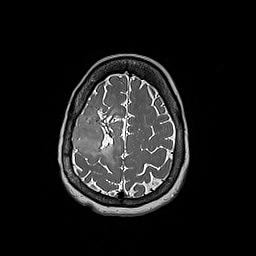
Brain MRI from a brain-tumour surgery series, one axial slice. Position 54 of 192 along the scan axis. 256 × 256 image matrix. From the clinical record (not read from this slice): histopathology: Oligodendroglioma; WHO grade: 3; IDH mutation: yes; tumour location: Right Frontal.
Annotated regions visible in this slice (outlined manually by an expert reader):
- tumour: bounding box [x1, y1, x2, y2] px = [72, 113, 104, 154]